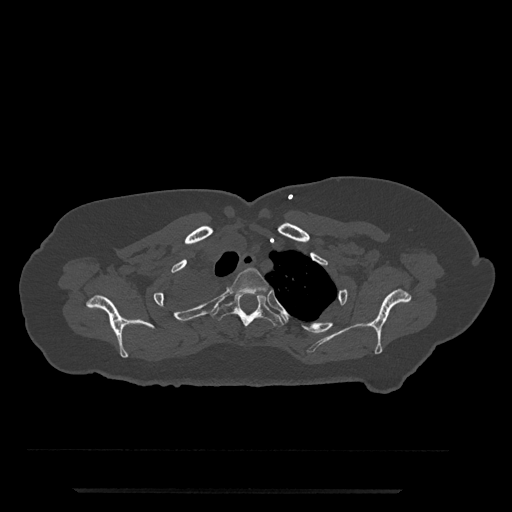
CT including the spine, one axial slice; position 646 of 797 along the scan axis; bone window (W 1800 / L 400 HU); 512 × 512 image matrix. Patient: female, 51 years. Case-level facts recorded for this patient, not image findings: primary cancer: neuro; vertebrae with lytic lesions (as recorded): T8.
Annotated regions visible in this slice (semi-automatic segmentation, software-assisted and operator-edited):
- T2 vertebra: bounding box (x1, y1, x2, y2) in pixels: (228, 267, 269, 295)
- T3 vertebra: (195, 292, 284, 327)